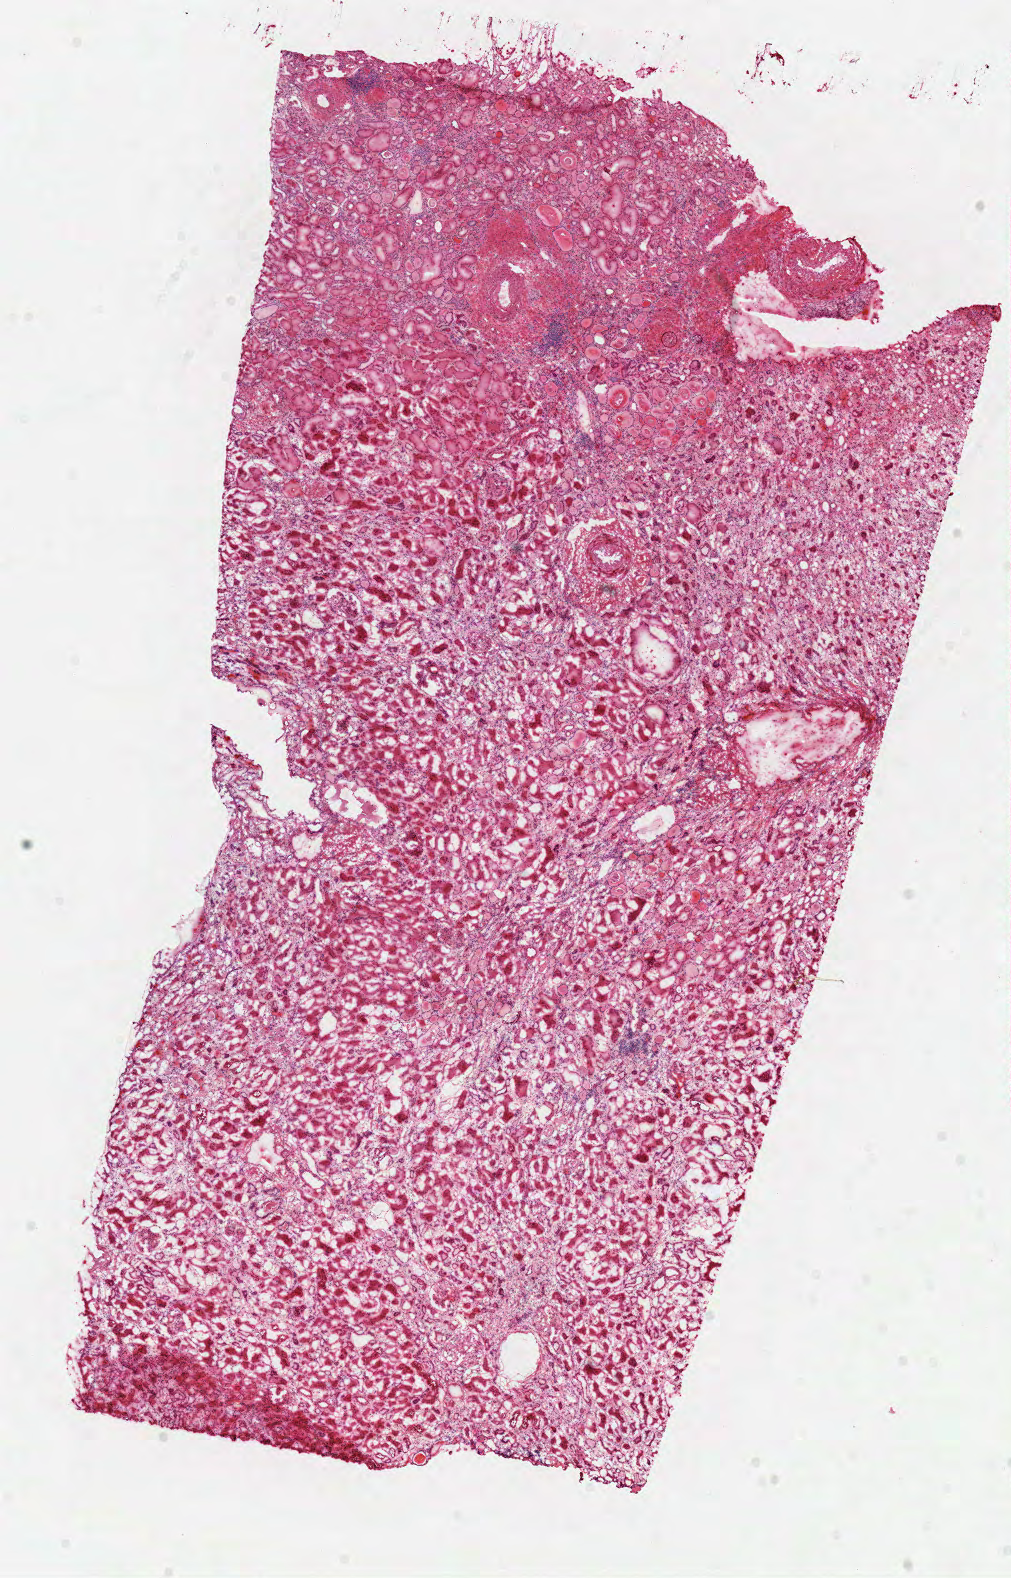
Whole-slide histology image, Hematoxylin and eosin (H&E) stained — shown as a low-resolution overview of the whole scanned area (about 8.0 x 12.4 mm, acquisition: 40x scan). Frozen section from the top of the tissue portion. Kidney, solid tissue normal (non-tumour tissue) sample. Male patient; age at initial diagnosis 69 years.
This section: solid tissue normal (non-tumour) sample from the same patient. Patient diagnosis: Papillary adenocarcinoma, NOS.